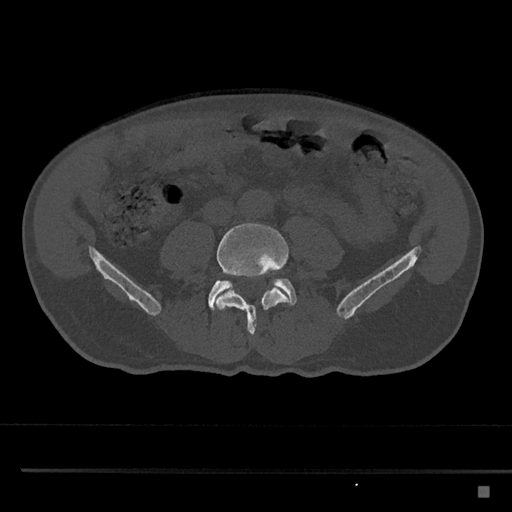
CT including the spine, one axial slice. Position 616 of 797 along the scan axis. Reconstruction kernel Br40s/3. Bone window (W 1800 / L 400 HU). 0.5 mm slice thickness. 512 × 512 image matrix. Patient: male, 59 years. From the clinical record (not read from this slice): primary cancer: prostate.
Annotated regions visible in this slice (semi-automatic segmentation, software-assisted and operator-edited):
- L4 vertebra: bounding box (x1, y1, x2, y2) in pixels: (216, 223, 289, 334)
- L5 vertebra: (208, 278, 297, 311)